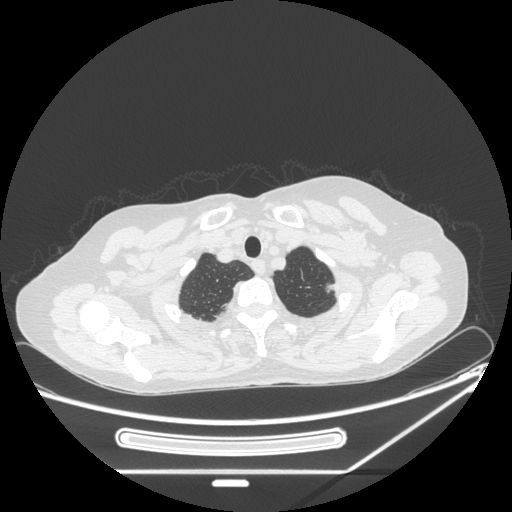
Chest CT, one axial slice. Slice 217 of 250 in the series (ordered by position). Lung window (W 1500 / L -600 HU). 1.25 mm slice thickness. 512 × 512 image matrix, field of view 409 × 409 mm. Patient: female, 57 years. From the clinical record (not read from this slice): clinical TNM (as recorded): T1c N0 M0; histopathological grade: G2-3.
Outlined on this slice (bounding box drawn by a radiologist):
- lung tumour (recorded histology: adenocarcinoma): bounding box (x1, y1, x2, y2) in pixels: (319, 278, 342, 299)